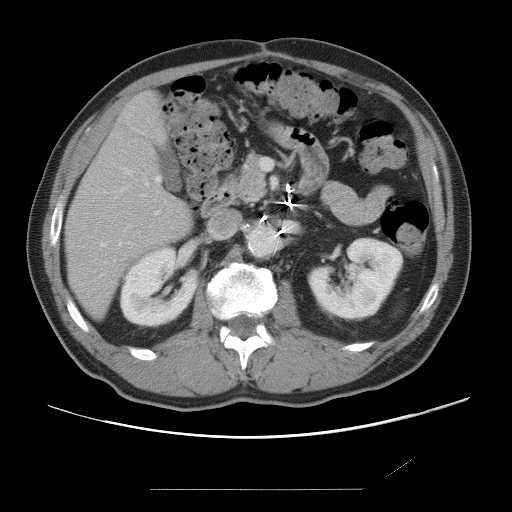
Contrast-enhanced abdominal CT, one axial slice; position 32 of 87 along the scan axis; intravenous contrast given; soft-tissue window (W 400 / L 40 HU); 5 mm slice thickness; 512 × 512 image matrix, field of view 406 × 406 mm. Male patient, age 74 years. From the clinical record (not read from this slice): diagnosis: colorectal cancer liver metastases, imaged before liver resection; multiple liver metastases: yes; largest metastasis: 1.1 cm; chemotherapy before resection: yes.
Structures marked on this image (outlined manually by an expert reader):
- hepatic veins: bounding box <101,170,130,247> (left, top, right, bottom; pixels)
- liver: <67,95,192,315>
- planned liver remnant (the part of the liver to remain after resection): <67,95,191,315>
- portal vein (with intrahepatic branches): <142,180,160,215>
- liver metastasis: <74,257,82,265>